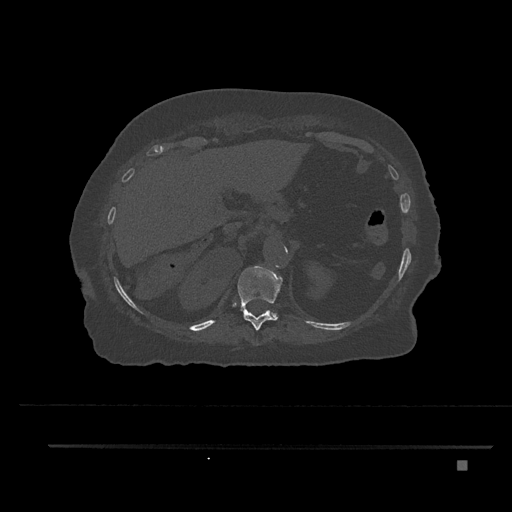
CT including the spine, one axial slice; 120 kVp; bone window (W 1800 / L 400 HU); 512 × 512 image matrix, field of view 437 × 437 mm. Patient: female, 76 years. From the clinical record (not read from this slice): primary cancer: lung; vertebrae with lytic lesions (as recorded): T11, L3.
Outlined on this slice (semi-automatically segmented with operator editing):
- T11 vertebra: bounding box [x1, y1, x2, y2] px = [235, 266, 283, 330]
- T12 vertebra: [274, 313, 276, 316]